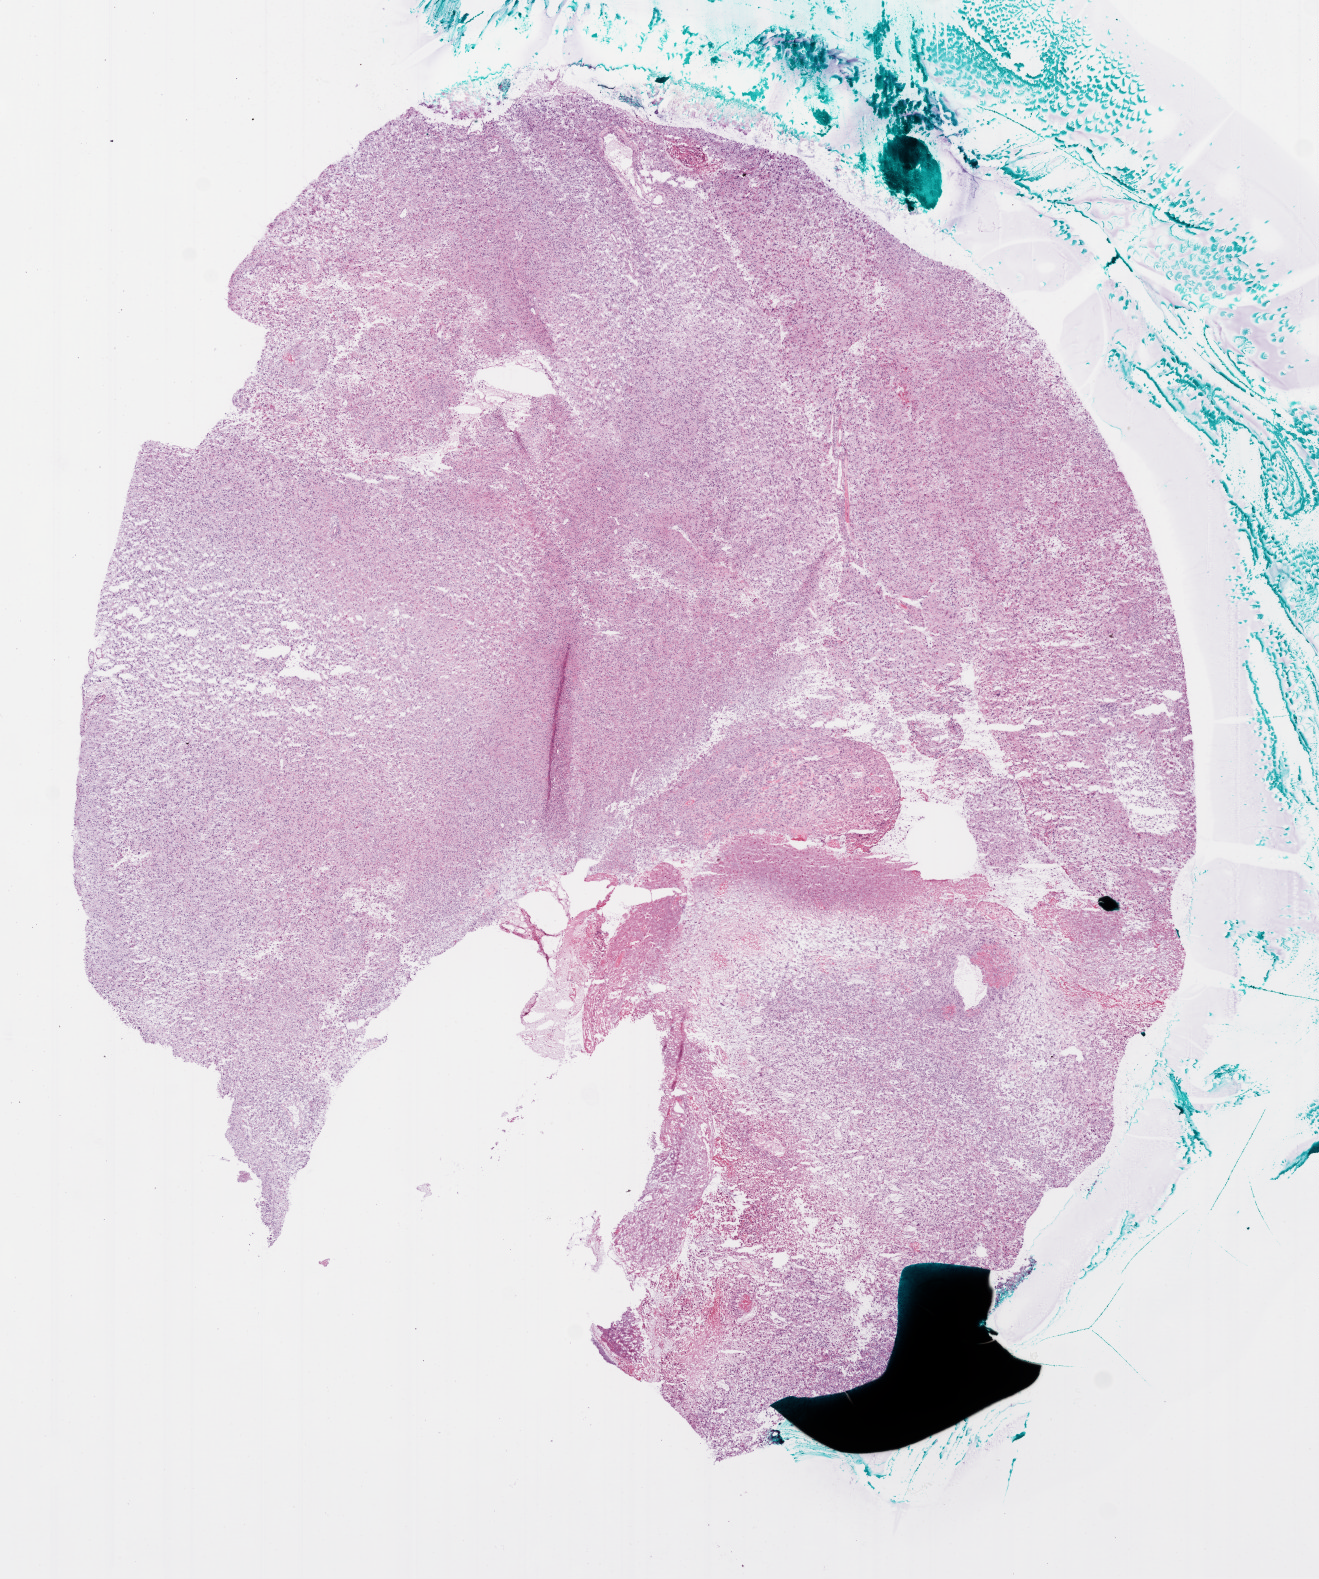
H&E-stained whole-slide image — a low-resolution overview of the entire scanned area, about 10.6 x 12.7 mm (slide scanned at 20x); frozen section from the bottom of the tissue portion; brain, primary tumour sample. Female patient; age at initial diagnosis 73 years. Slide review estimates, as recorded: tumour cells 80%, tumour nuclei 90%, normal cells 0%, stromal cells 0%, necrosis 20%. Inflammatory infiltration, as recorded: neutrophil infiltration 100%.
* diagnosis: Glioblastoma